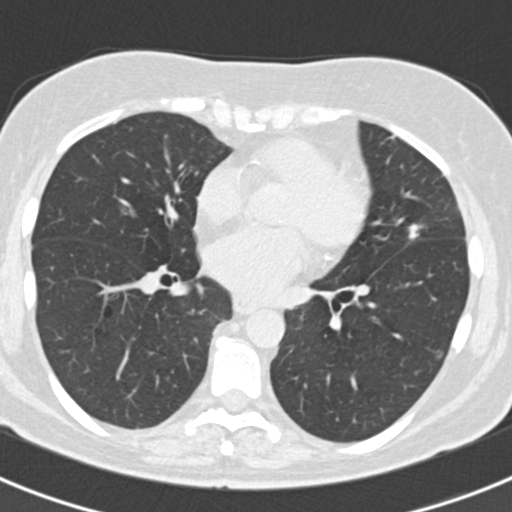
Low-dose screening chest CT, axial slice. First (baseline) screen. Lung window (W 1500 / L -600 HU). 2 mm slice thickness. Standard (soft-tissue) reconstruction kernel (B30f). 120 kVp. Slice 110 of 184 in the series. 512 × 512 image matrix. Female, age 60 years at enrolment. Current smoker at enrolment.
Expert-annotated lung lesion, bounding box <397,216,433,250> (left, top, right, bottom; pixels). The screening reader recorded 3 non-calcified nodules or masses ≥4 mm on this exam; which of them this box marks is not recorded. Official screen result: positive, change unspecified: nodule(s) >= 4 mm or enlarging nodule(s), mass(es), or other non-specific abnormalities suspicious for lung cancer.